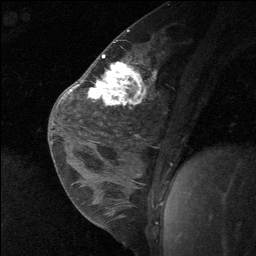
Breast MRI (dynamic contrast-enhanced), one sagittal slice; position 34 of 64 along the scan axis; dynamic contrast-enhanced study with each time point stored as its own series, time point 2 of 3 at this slice position (early post-contrast, ordered by acquisition time); 1.5 T; TE 4.8 ms, TR 27 ms; 2 mm slice thickness; 256 × 256 image matrix, field of view 180 × 180 mm. Female patient, age 26 years. Case-level facts recorded for this patient, not image findings: setting: breast cancer imaged before/during neoadjuvant chemotherapy; receptor status: HR-positive, HER2-negative.
Annotated regions visible in this slice (semi-automatic segmentation, software-assisted and operator-edited):
- analysis volume of interest (the breast-tissue region the enhancement analysis was run in; not a lesion): bounding box <86,43,134,138> (left, top, right, bottom; pixels)
- tumour enhancement mask (voxels above the 90 % enhancement threshold inside the analysis volume of interest): <88,62,126,103>